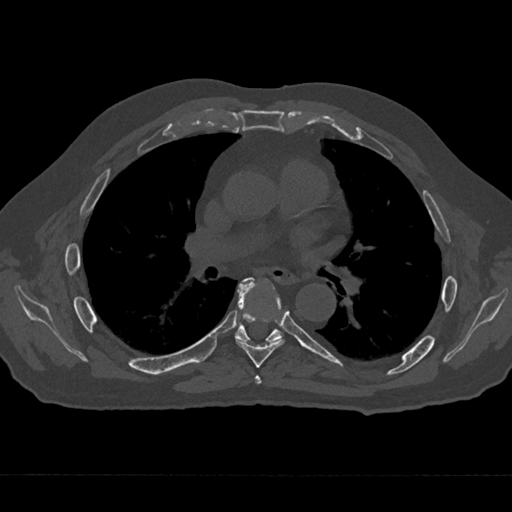
CT including the spine, one axial slice; slice 401 of 797 in the series (ordered by position); 120 kVp; bone window (W 1800 / L 400 HU); 0.5 mm slice thickness; 512 × 512 image matrix, field of view 377 × 377 mm. Male patient, age 75 years. From the clinical record (not read from this slice): primary cancer: renal; vertebrae with lytic lesions (as recorded): T4.
Structures marked on this image (semi-automatically segmented with operator editing):
- T5 vertebra: bounding box <255,375,261,385> (left, top, right, bottom; pixels)
- T6 vertebra: <235,277,285,368>
- T7 vertebra: <235,278,283,343>